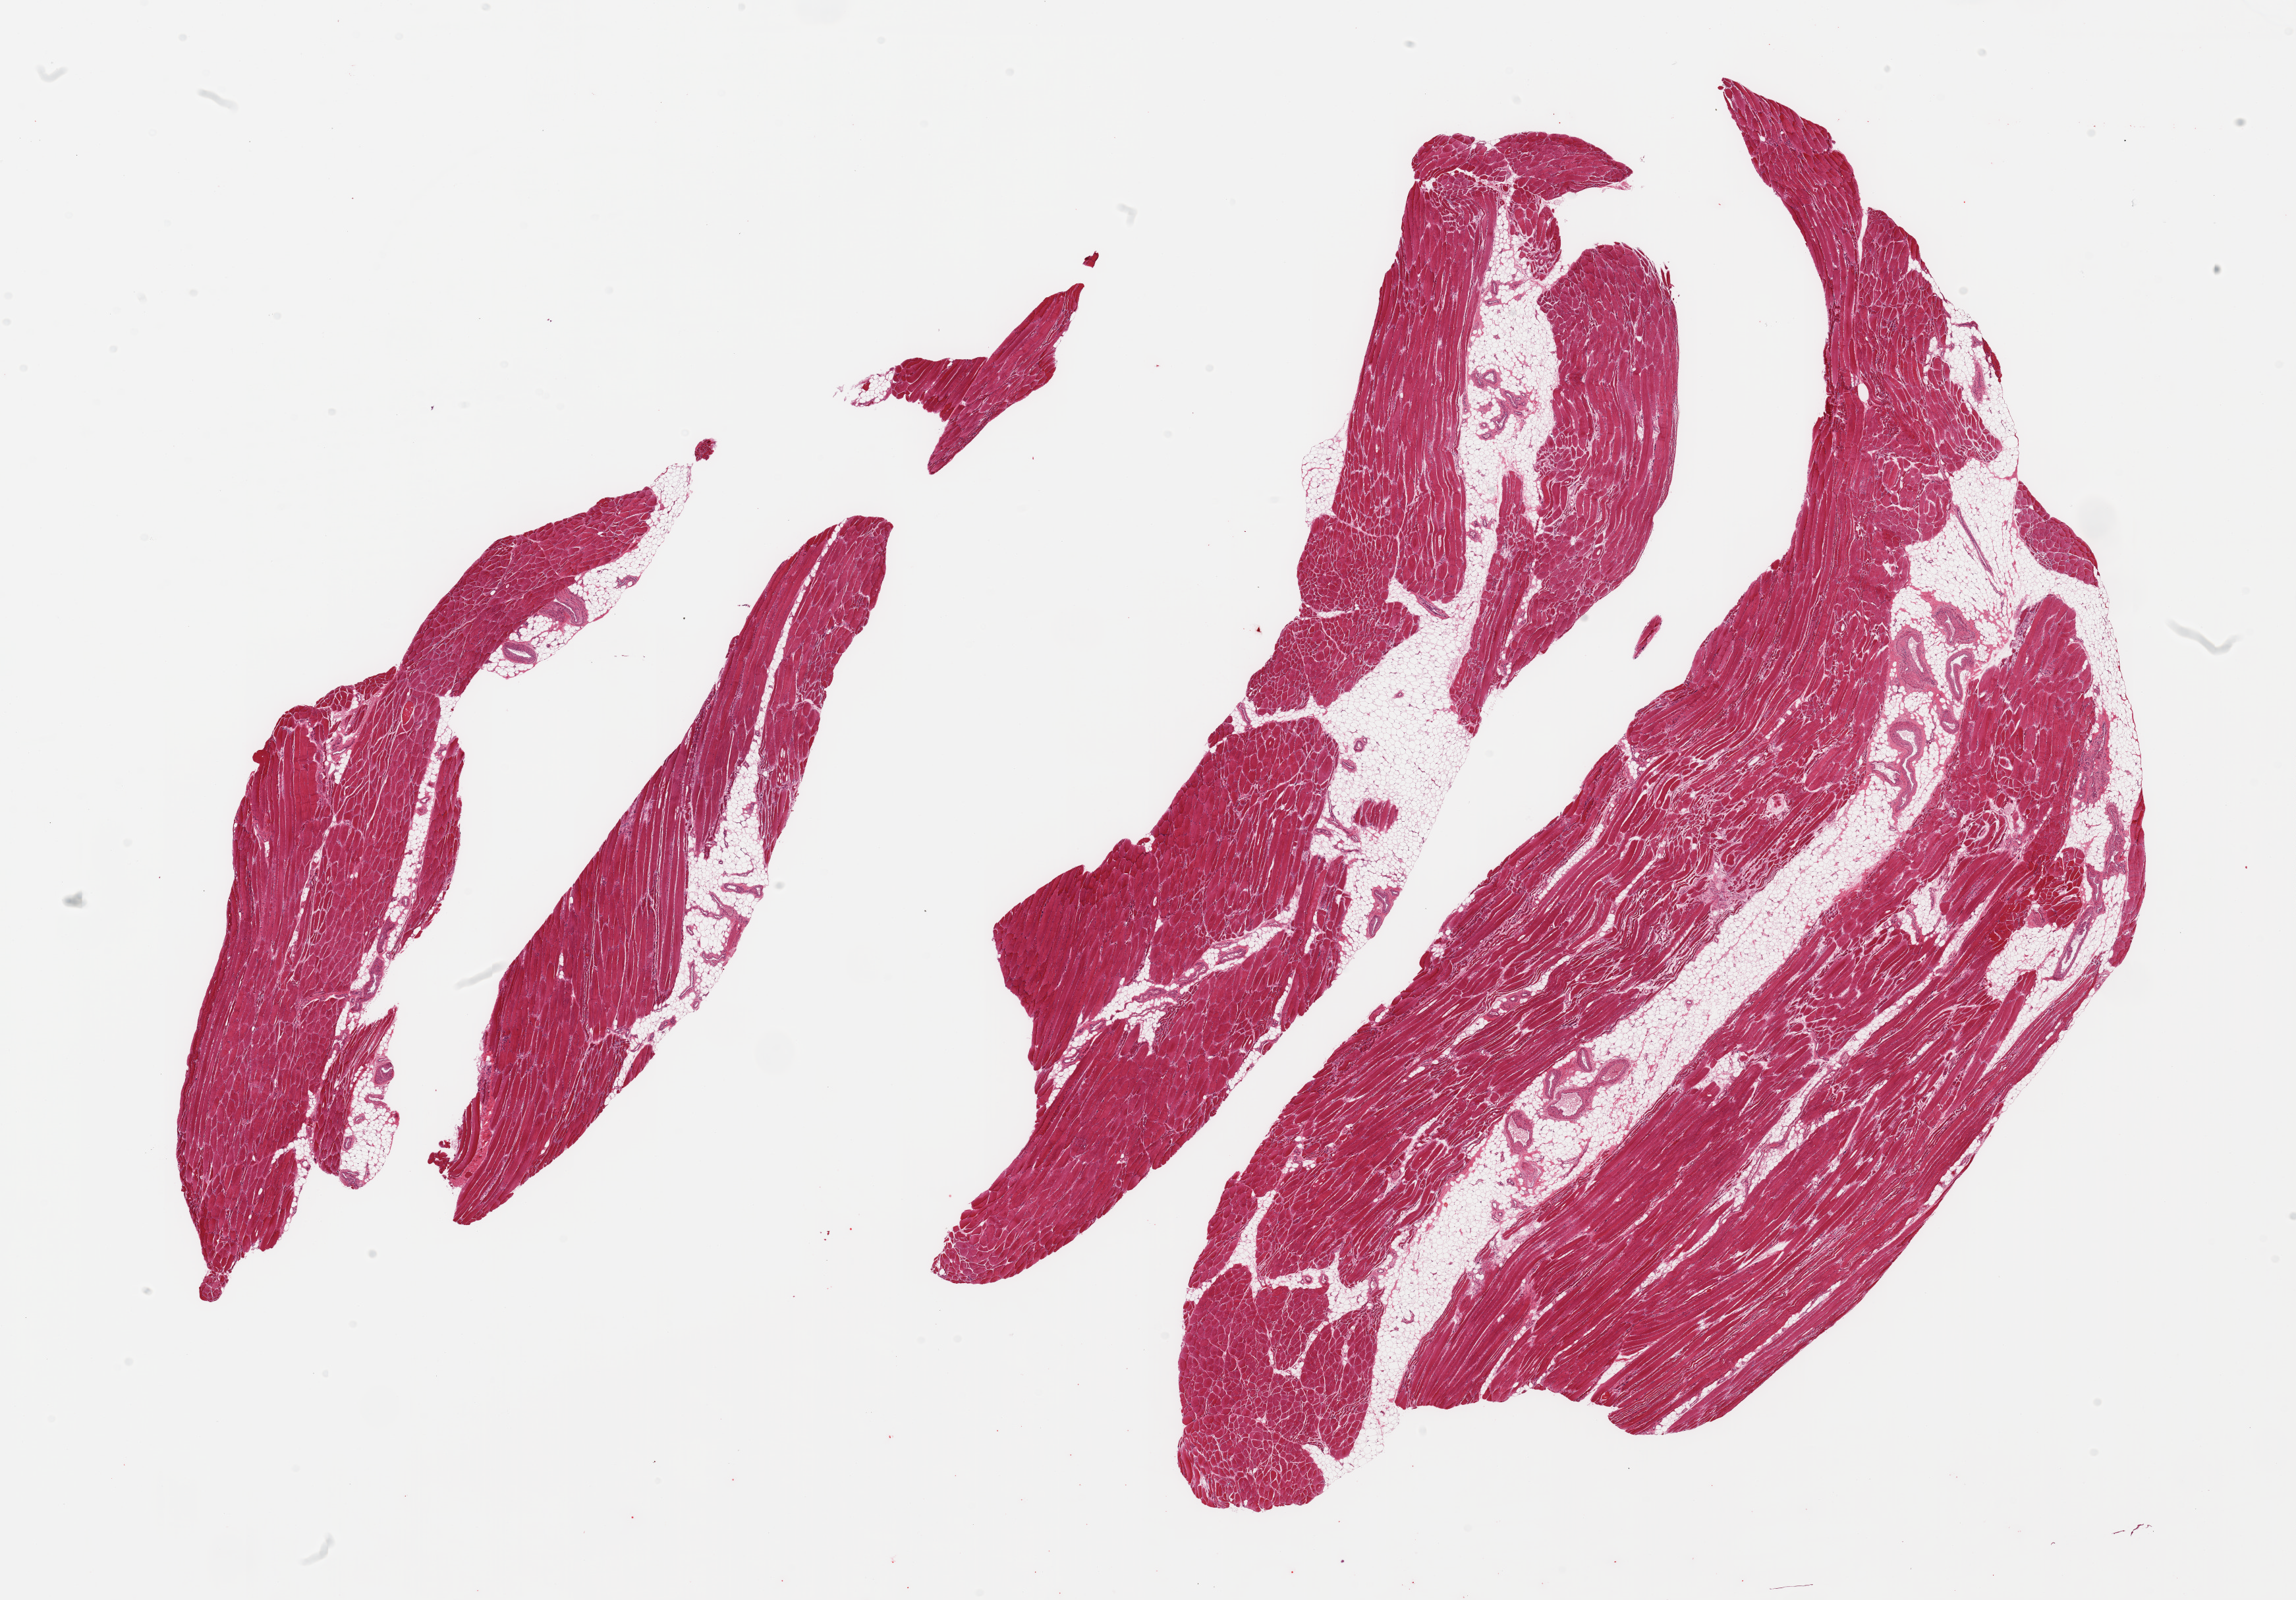
Whole-slide image, haematoxylin and eosin stain, shown as a low-resolution overview of the whole scanned area (about 27.6 x 19.2 mm, slide scanned at 20x); PAXgene-fixed, paraffin-embedded tissue; target tissue: skeletal muscle; donor tissue sample.
Review note (as recorded): 2 pieces; includes up to 20% internal fat, some atrophy.